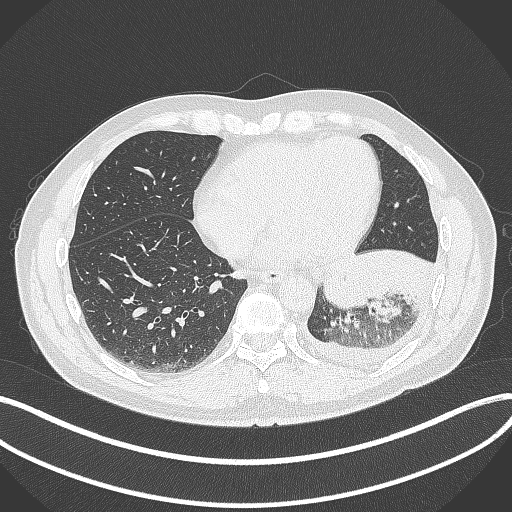
Chest CT, one axial slice. Position 117 of 342 along the scan axis. Reconstruction kernel B70f. 120 kVp. Lung window (W 1500 / L -600 HU). 1 mm slice thickness. 512 × 512 image matrix, field of view 400 × 400 mm. Male patient, age 58 years. From the clinical record (not read from this slice): clinical TNM (as recorded): T3 N1 M1b; histopathological grade: G3.
Outlined on this slice (bounding box drawn by a radiologist):
- lung tumour (recorded histology: small cell carcinoma): box from (x=321, y=249) to (x=373, y=318) px